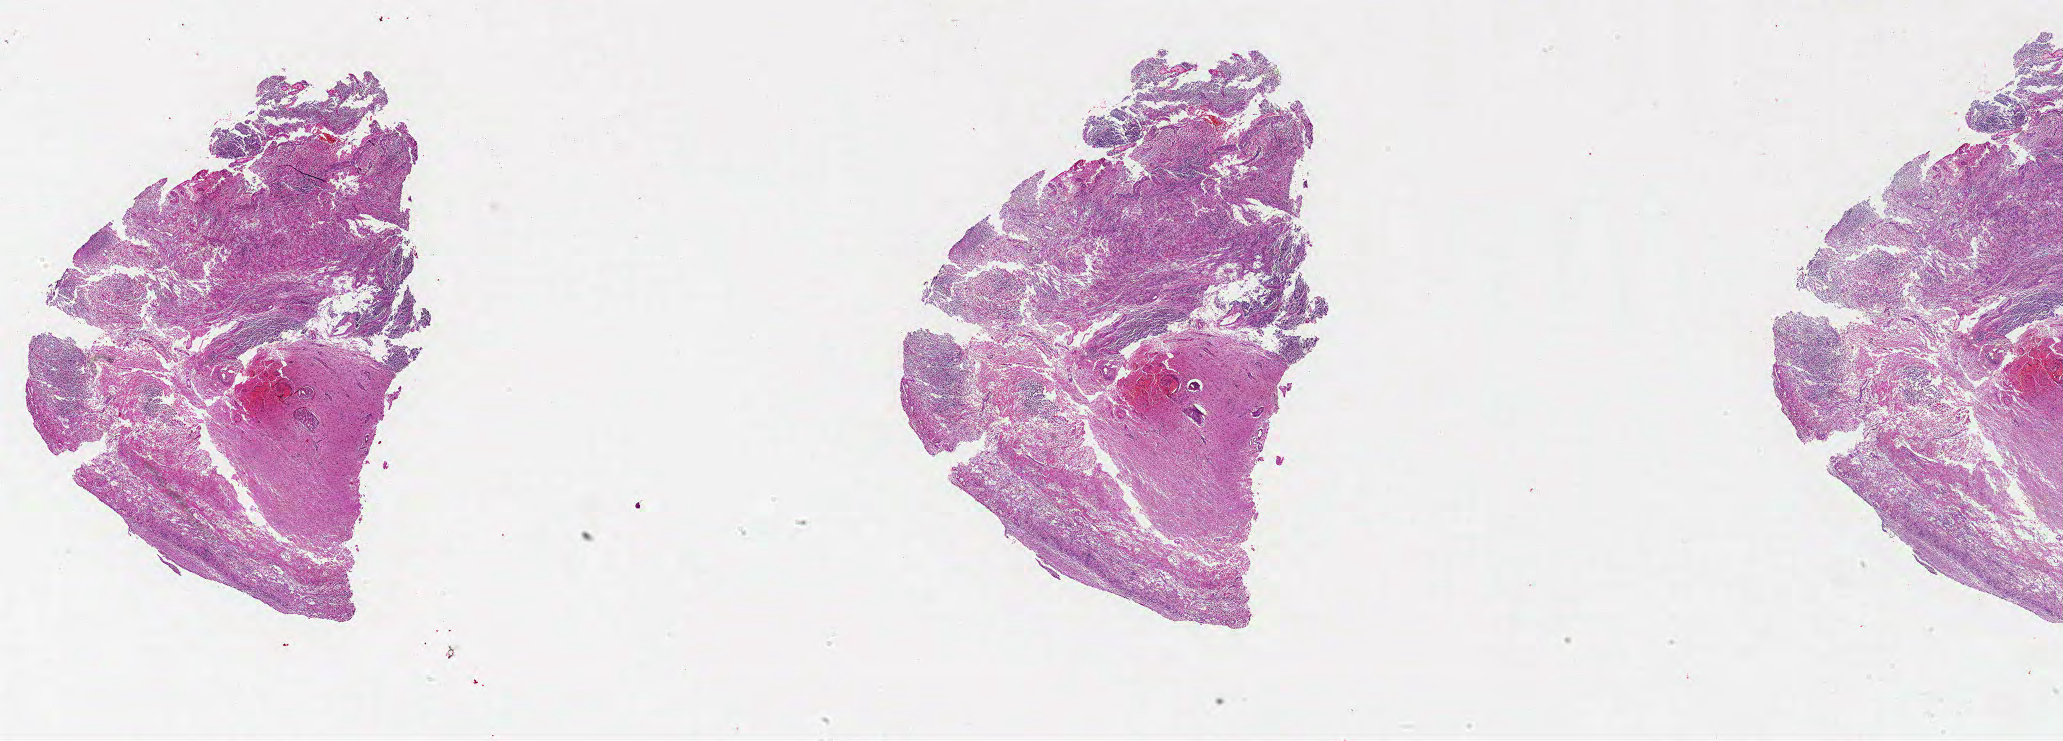
Whole-slide histology image, Hematoxylin and eosin (H&E) stained, whole scanned area (about 33.0 x 11.8 mm, acquisition: 20x scan) shown as a low-resolution overview, FFPE section, brain, primary tumour sample. Female, age 47 years at initial diagnosis.
- pathologic diagnosis: Glioblastoma